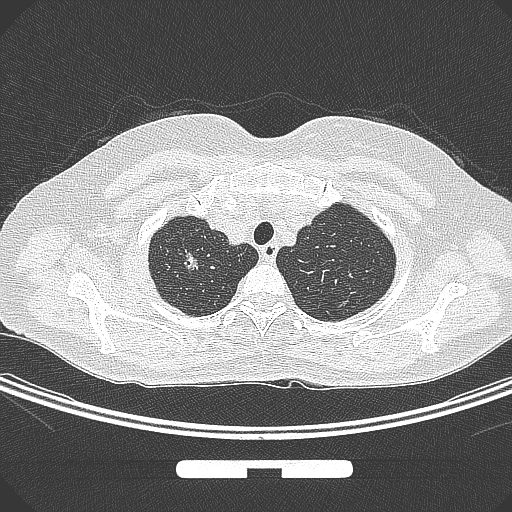
Chest CT, one axial slice. Position 256 of 295 along the scan axis. Lung window (W 1500 / L -600 HU). 1 mm slice thickness. 512 × 512 image matrix, field of view 369 × 369 mm. Patient: female, 58 years. From the clinical record (not read from this slice): clinical TNM (as recorded): T1b N0 M0.
Structures marked on this image (rectangle marked by the reading radiologist):
- lung tumour (recorded histology: adenocarcinoma): bounding box <177,247,201,276> (left, top, right, bottom; pixels)